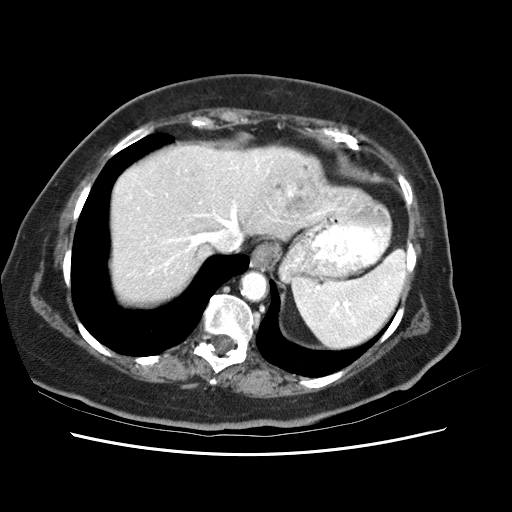
Contrast-enhanced abdominal CT (liver protocol), one axial slice. Slice 52 of 62 in the series (ordered by position). 120 kVp. Soft-tissue window (W 400 / L 40 HU). 2.5 mm slice thickness. 512 × 512 image matrix, field of view 340 × 340 mm. Case-level facts recorded for this patient, not image findings: diagnosis: hepatocellular carcinoma (patient treated with transarterial chemoembolisation; whether this scan precedes or follows treatment is not stated here); TNM stage (as recorded): Stage-I; Child-Pugh class: B; tumour nodularity: uninodular.
Annotated regions visible in this slice (semi-automatic segmentation, software-assisted and operator-edited):
- abdominal aorta: bounding box <242,273,266,299> (left, top, right, bottom; pixels)
- liver parenchyma outside the tumour (the mass and vessels are separate outlines, so this box may not span the whole liver): <116,146,364,288>
- mass: <267,153,316,213>
- liver vessels: <137,177,311,229>